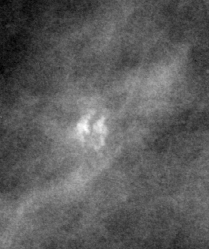
Region of interest cut from a scanned film mammogram (one marked finding), right breast, MLO view.
- Marked abnormality: calcifications, morphology pleomorphic, distribution clustered; BI-RADS assessment category 2; benign without callback (not worked up further).